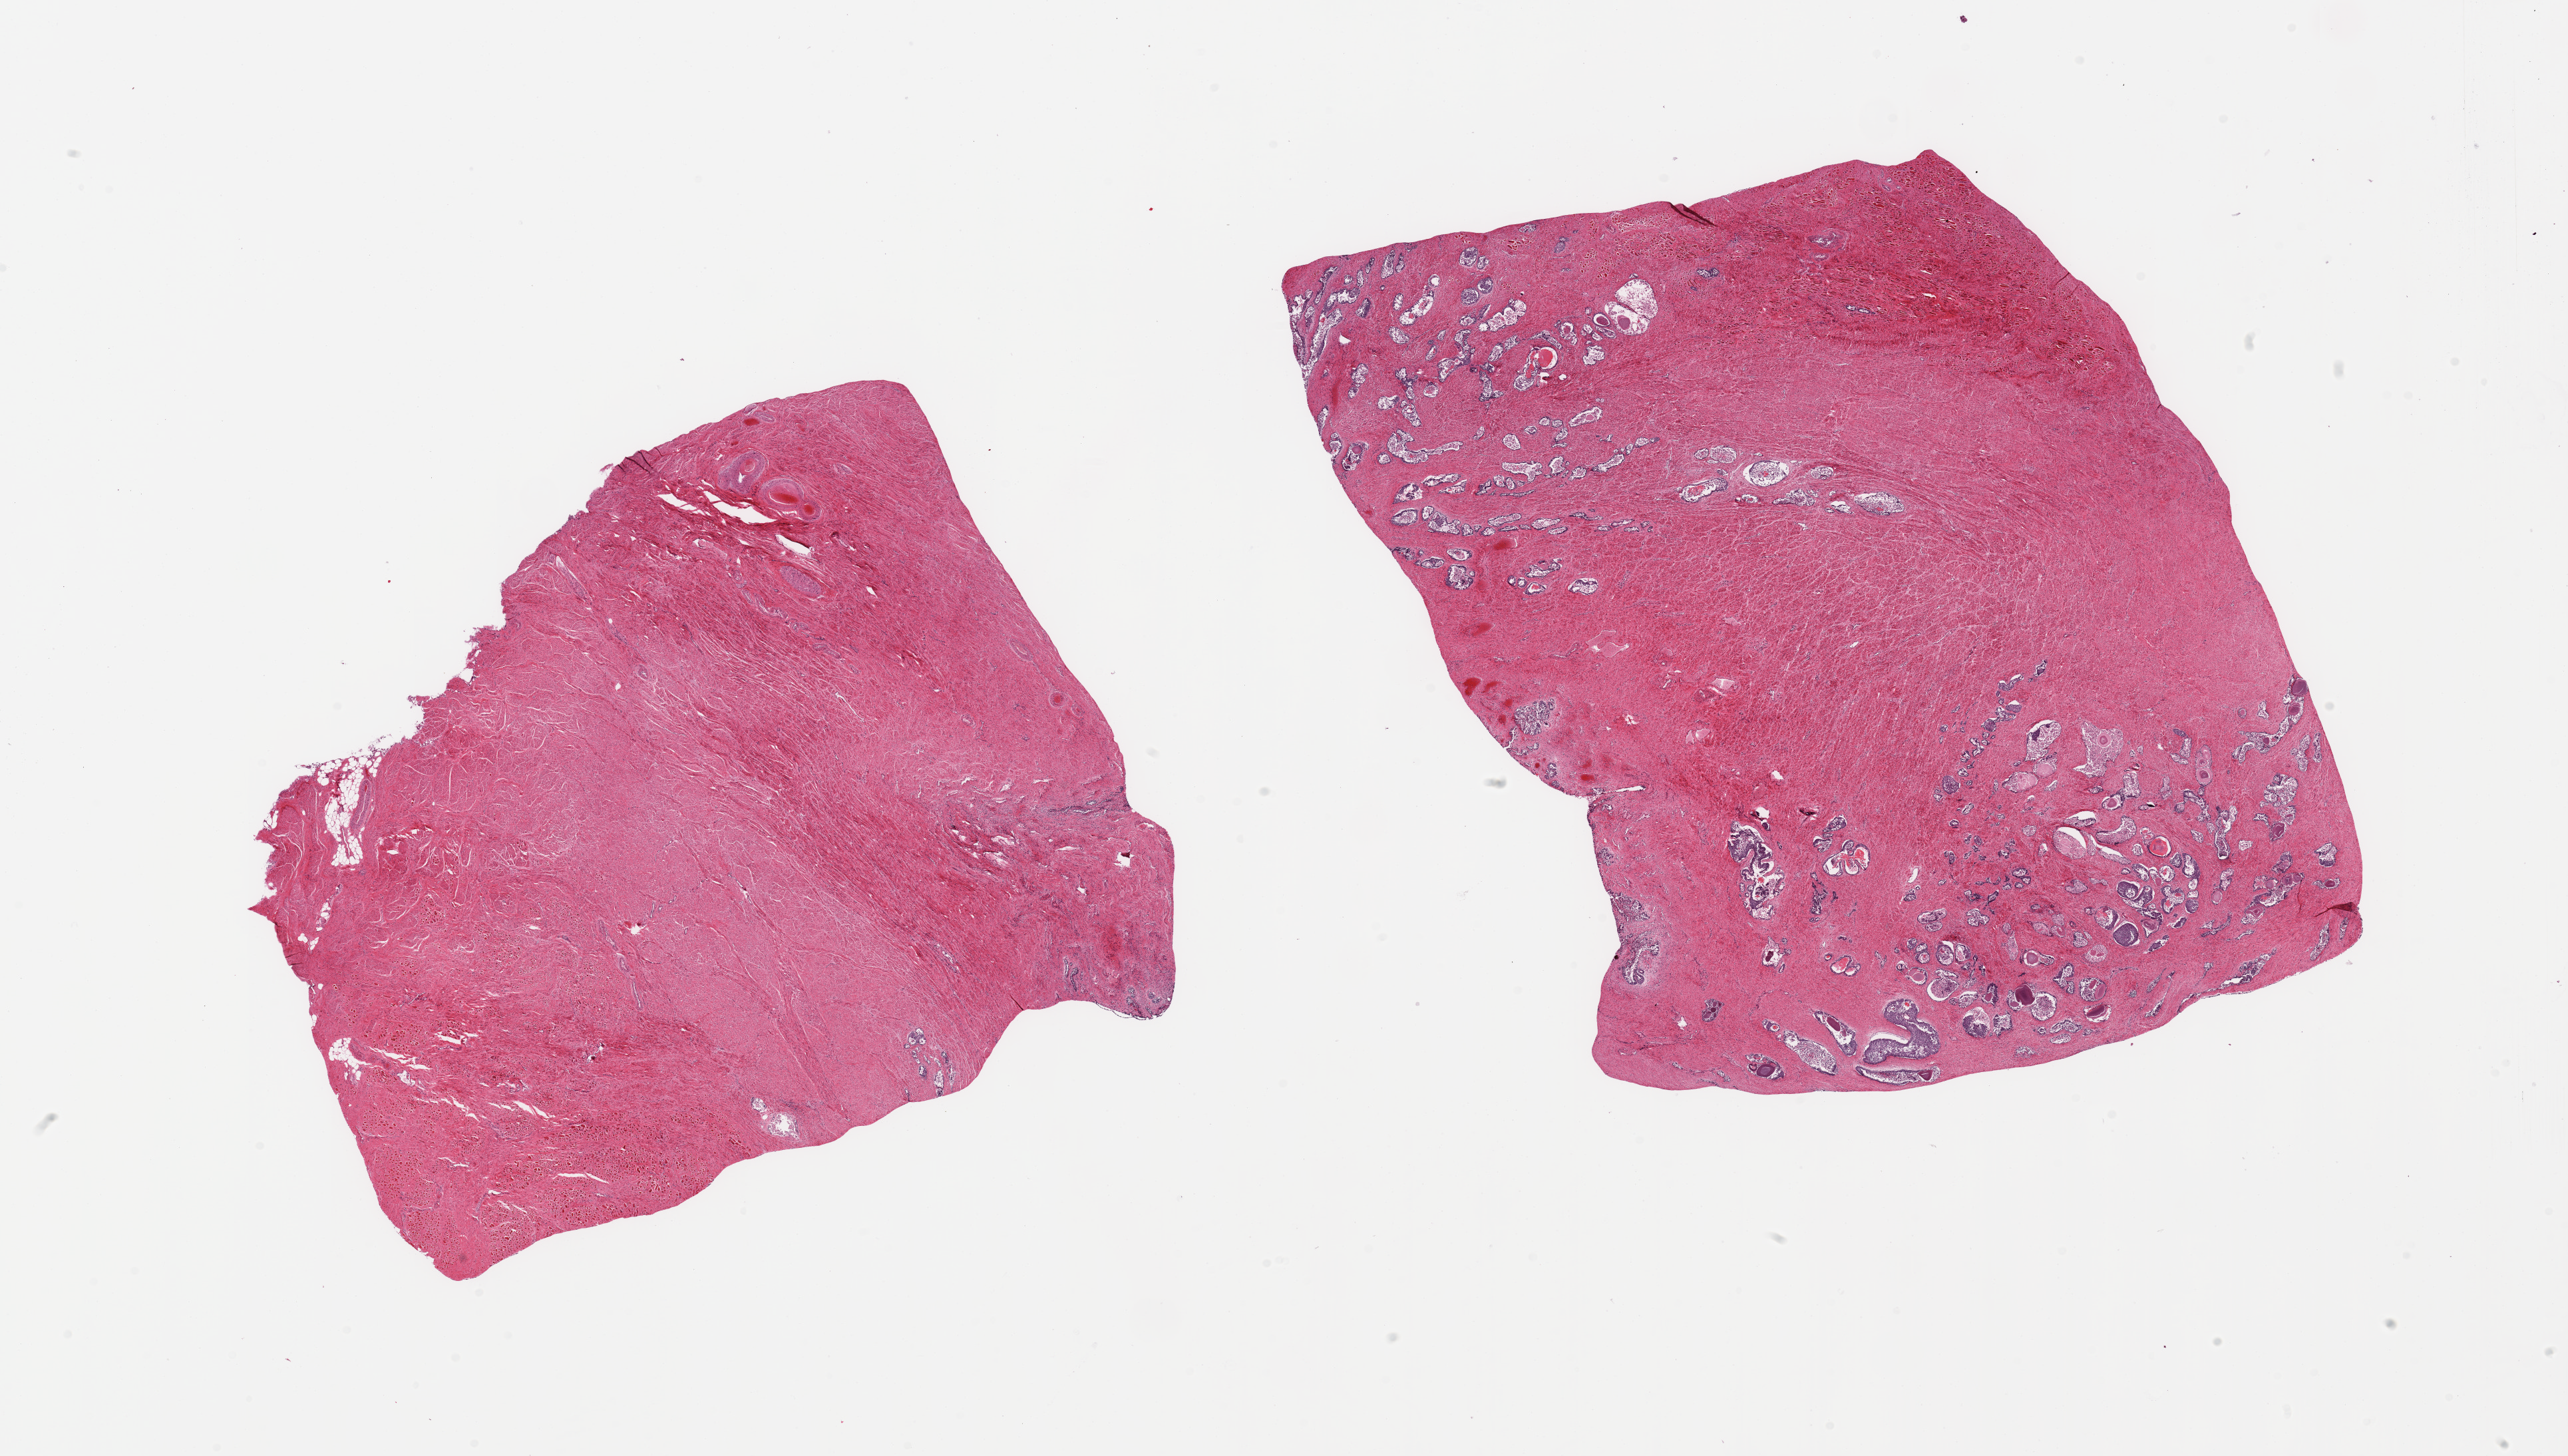
Whole-slide image, hematoxylin and eosin (H&E) stain — whole scanned area (about 30.5 x 17.3 mm) shown as a low-resolution overview; PAXgene-fixed, paraffin-embedded tissue; section of prostate (target tissue); tissue donor sample. Donor sex: male.
Reviewer comment on this tissue sample: 2 pieces; 1 largely fibromuscular stroma; other with autolyzed glands & muscular stroma.